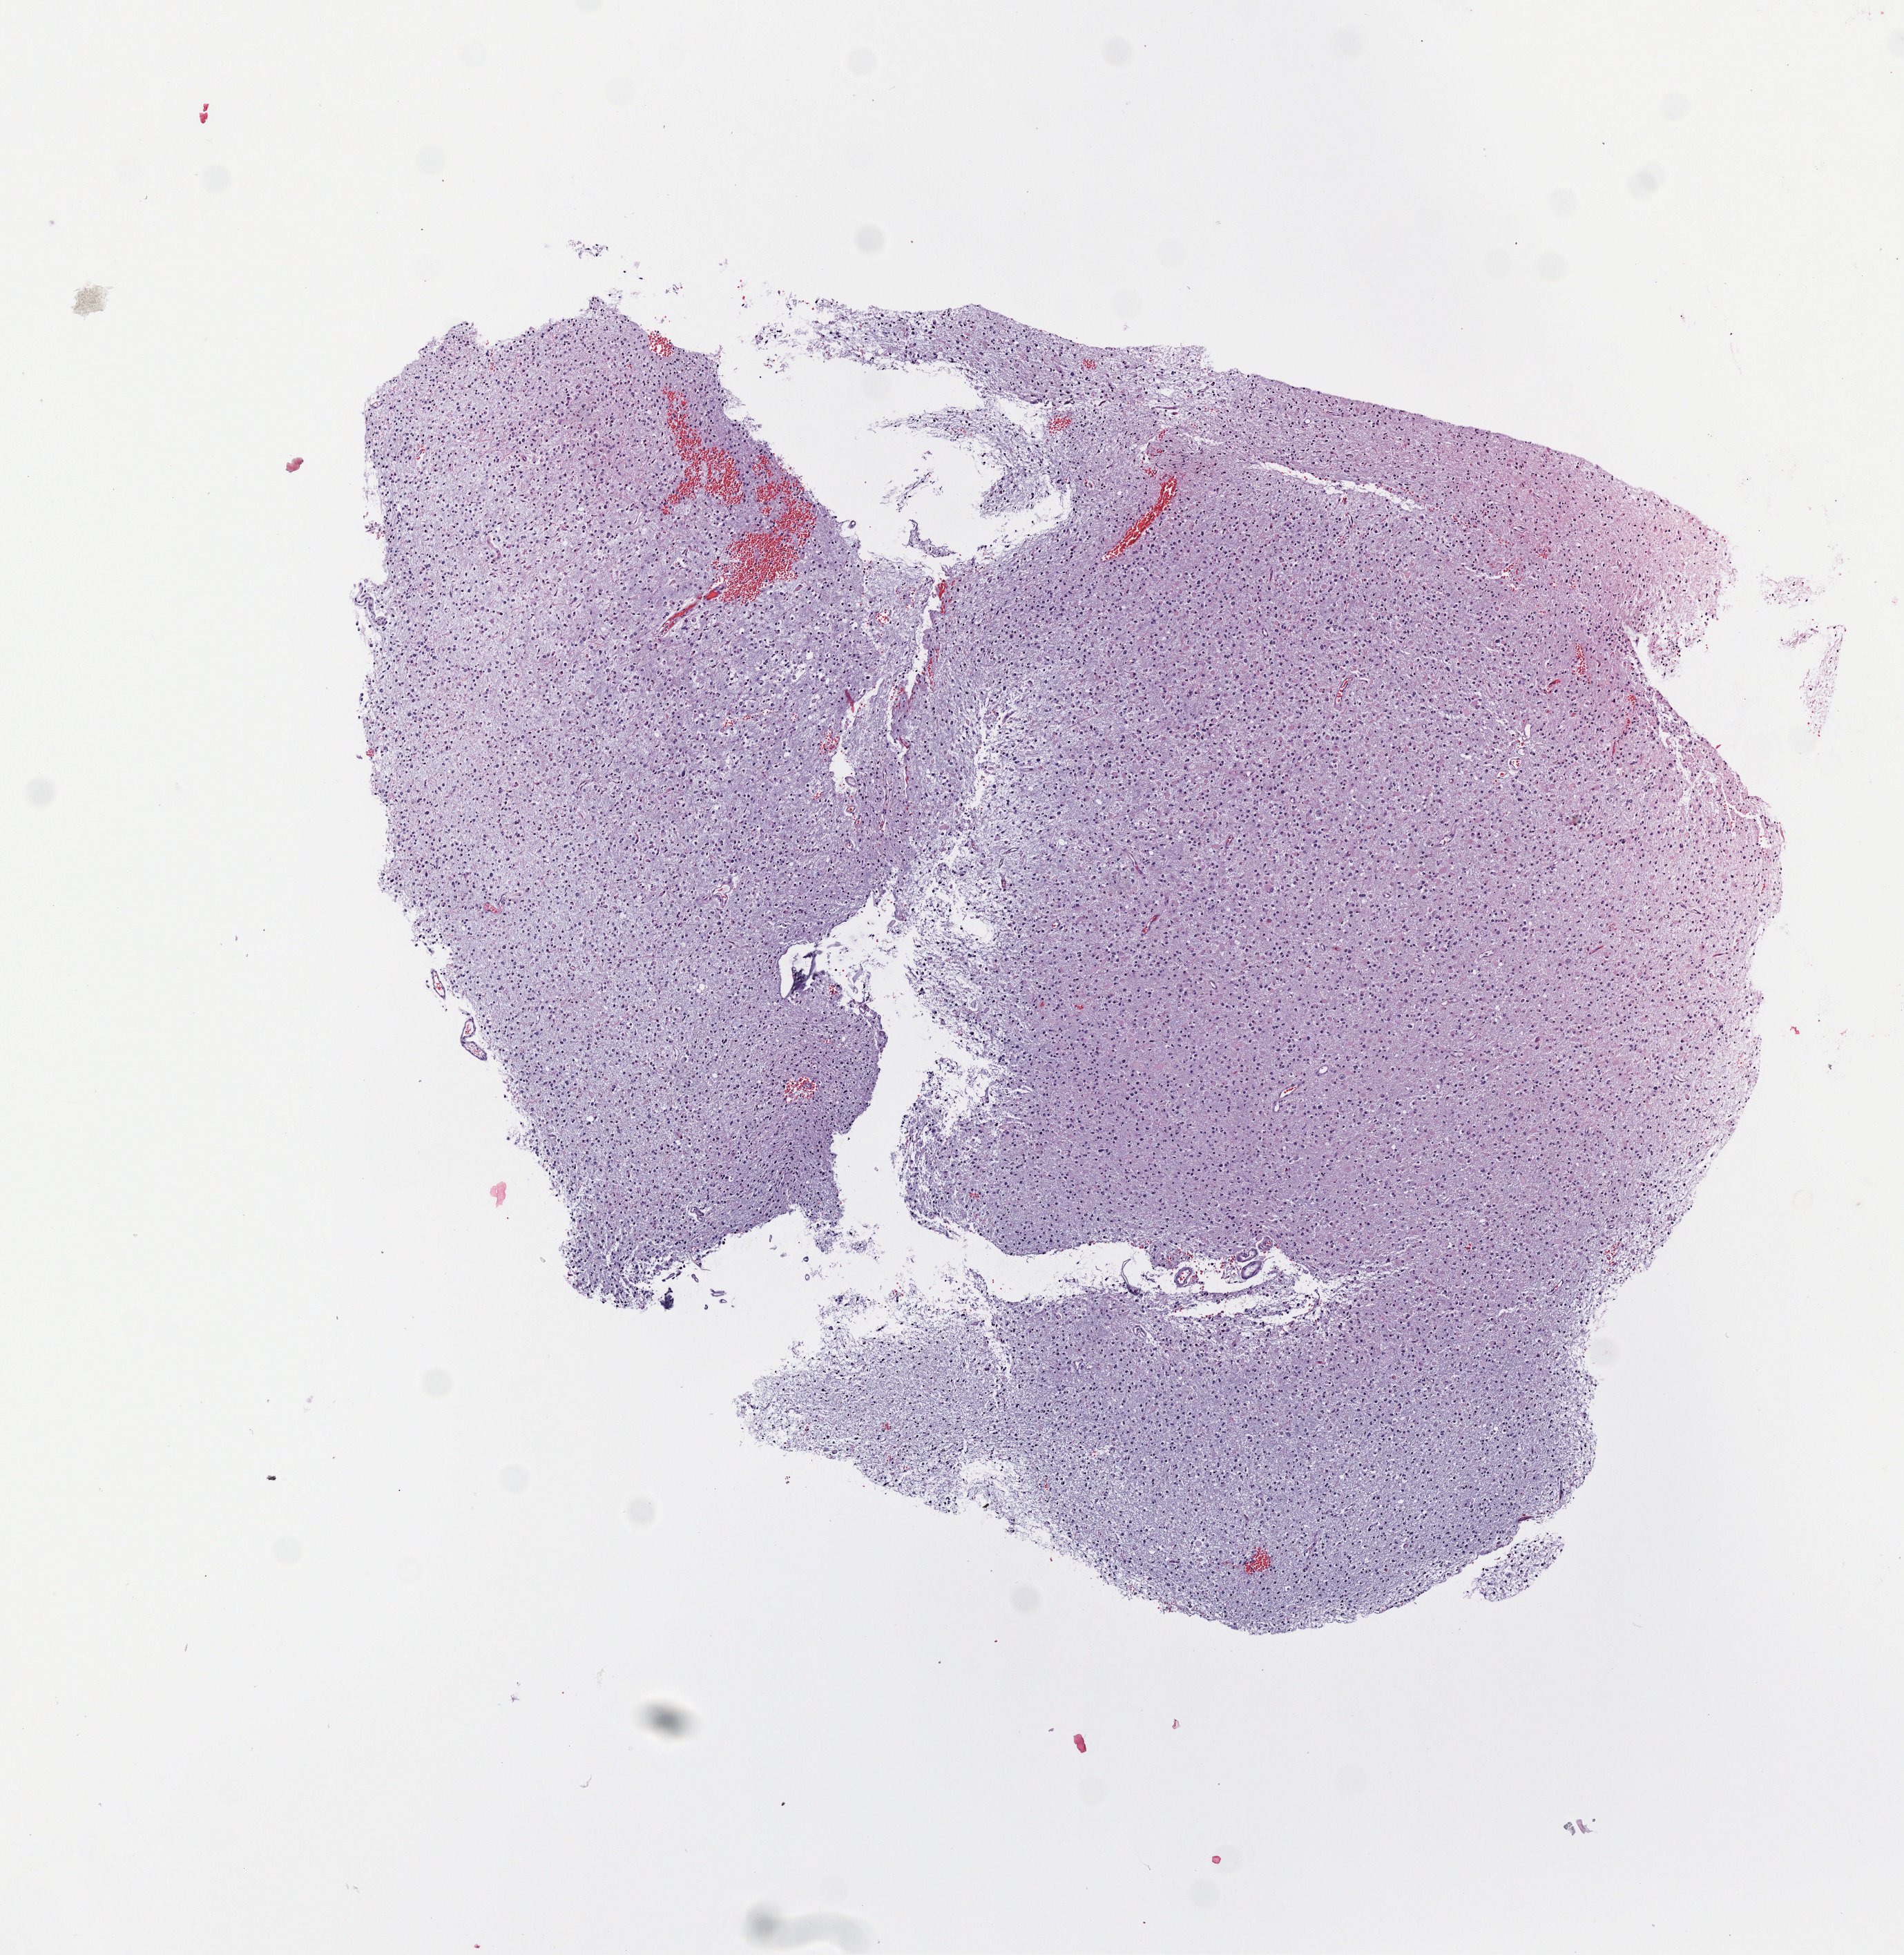
Digitized H&E-stained tissue section (whole slide), a low-resolution overview of the entire scanned area, about 5.6 x 5.7 mm (from a 40x scan). Formalin-fixed paraffin-embedded (FFPE) diagnostic section. Sample: primary tumour, brain. Female, age 69 years at initial diagnosis. Histologic grade: G2 (moderately differentiated).
Histologic diagnosis: Mixed glioma (cerebrum).